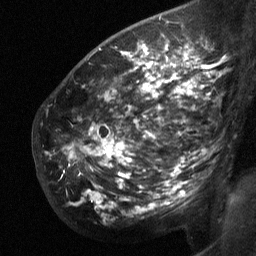
Breast MRI (dynamic contrast-enhanced), one sagittal slice. Slice 42 of 64 in the series (ordered by position). Dynamic contrast-enhanced study with each time point stored as its own series, time point 2 of 3 at this slice position (early post-contrast, ordered by acquisition time). 1.5 T. TE 4.8 ms, TR 27 ms. 2 mm slice thickness. 256 × 256 image matrix, field of view 200 × 200 mm. Patient: female, 50 years. From the clinical record (not read from this slice): setting: breast cancer imaged before/during neoadjuvant chemotherapy; receptor status: HER2-positive.
Outlined on this slice (semi-automatically segmented with operator editing):
- analysis volume of interest (the breast-tissue region the enhancement analysis was run in; not a lesion): bounding box [x1, y1, x2, y2] px = [49, 62, 212, 200]
- tumour enhancement mask (voxels above the 90 % enhancement threshold inside the analysis volume of interest): [96, 62, 194, 165]